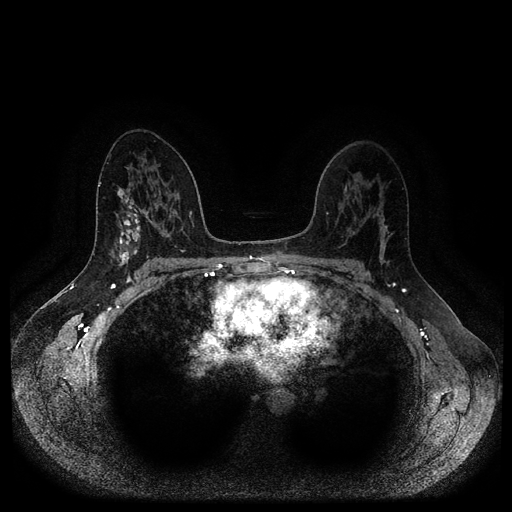
Breast MRI (dynamic contrast-enhanced, multi-phase), one axial slice; slice 61 of 116 in the series (ordered by position); dynamic contrast-enhanced series, time point 2 of 5 at this slice position (early post-contrast); 1.5 T; TE 2.6 ms, TR 5.3 ms; 2 mm slice thickness; 512 × 512 image matrix, field of view 360 × 360 mm. Female patient, age 45 years.
Structures marked on this image (semi-automatically segmented with operator editing):
- breast lesion (labelled benign in the annotation): bounding box (x1, y1, x2, y2) in pixels: (112, 205, 141, 268)